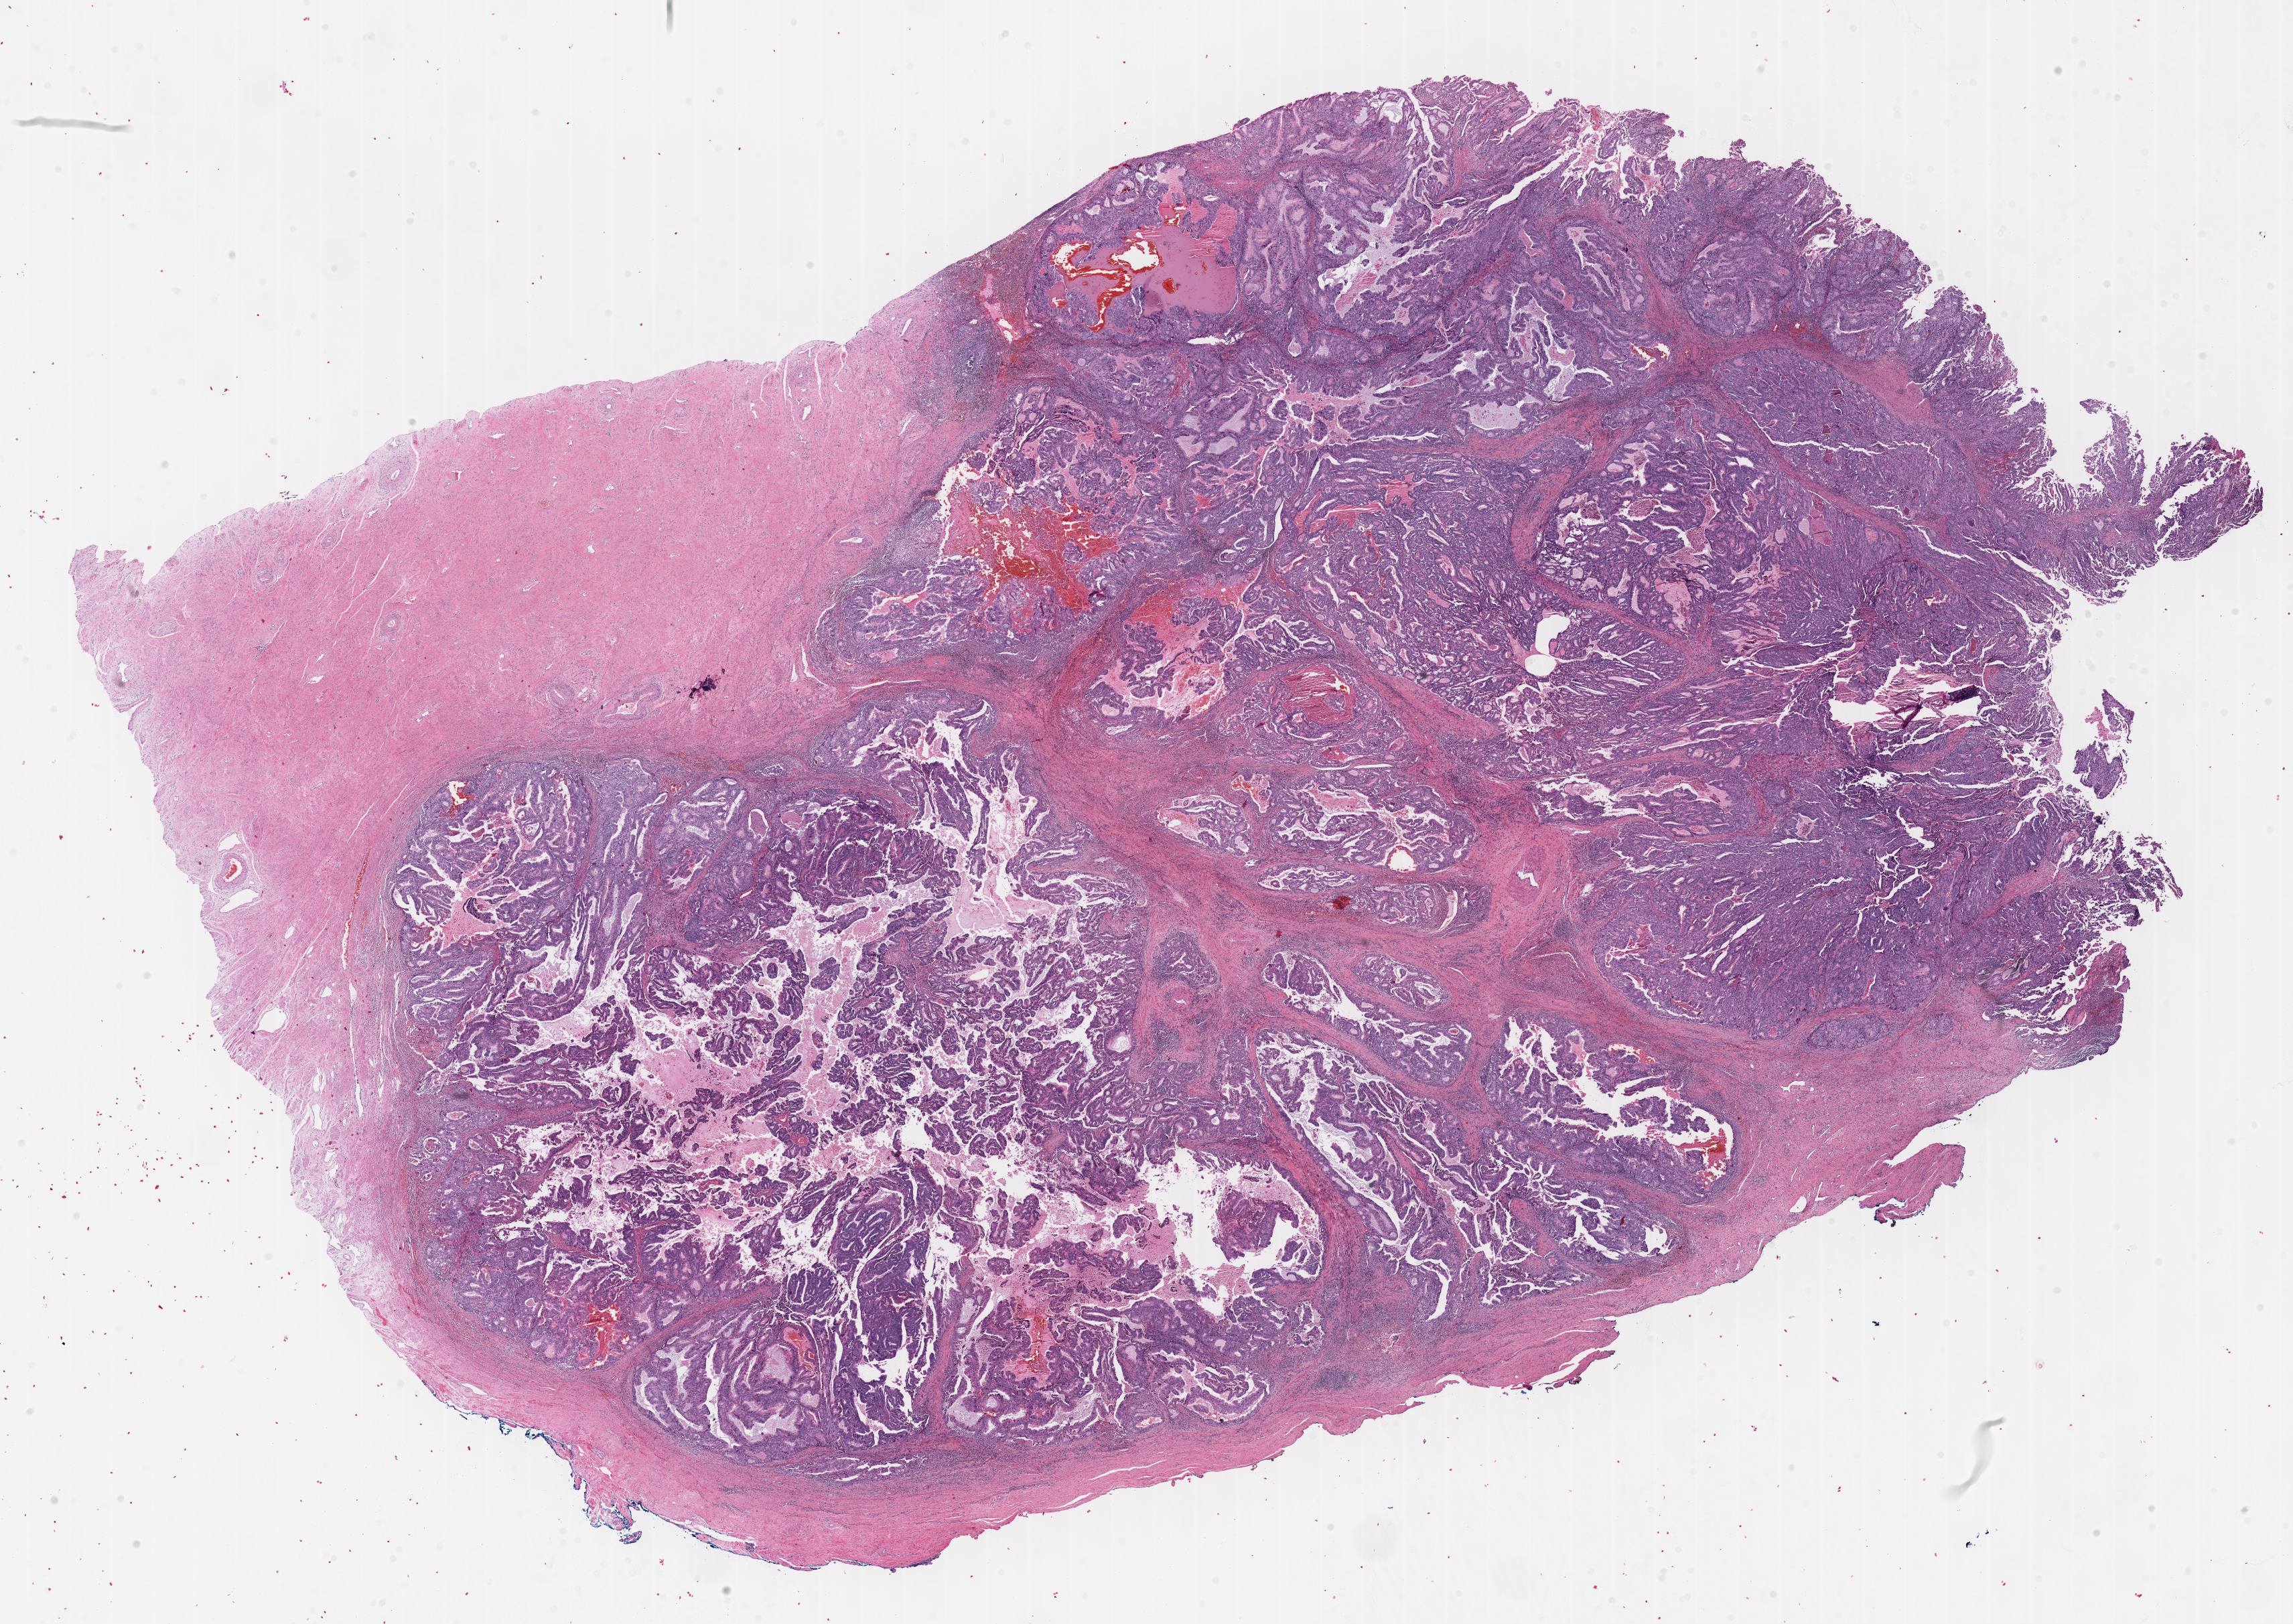
Digitized H&E-stained tissue section (whole slide) — whole scanned area (about 27.7 x 19.6 mm, slide scanned at 40x) shown as a low-resolution overview; FFPE section; sample: primary tumour, uterus. Female, age 71 years at initial diagnosis. Histologic grade: G3 (poorly differentiated).
Diagnosis: Endometrioid adenocarcinoma, NOS (endometrium). FIGO stage: IIIB.